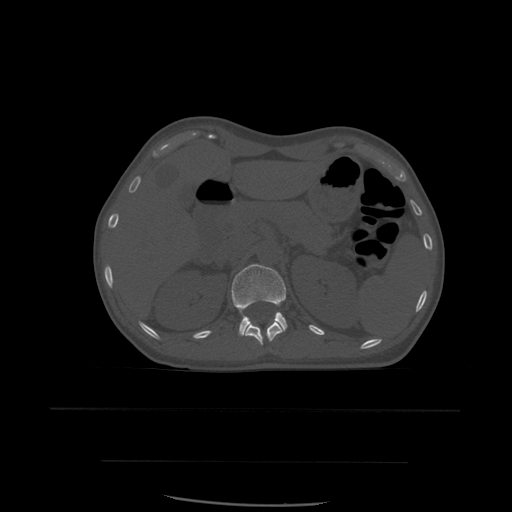
CT including the spine, one axial slice; position 261 of 574 along the scan axis; bone window (W 1800 / L 400 HU); 512 × 512 image matrix, field of view 392 × 392 mm. Patient age 48 years. From the clinical record (not read from this slice): primary cancer: lung; vertebrae with lytic lesions (as recorded): T11.
Annotated regions visible in this slice (semi-automatic segmentation, software-assisted and operator-edited):
- L1 vertebra: bounding box (x1, y1, x2, y2) in pixels: (231, 264, 288, 337)
- T12 vertebra: (245, 322, 283, 346)